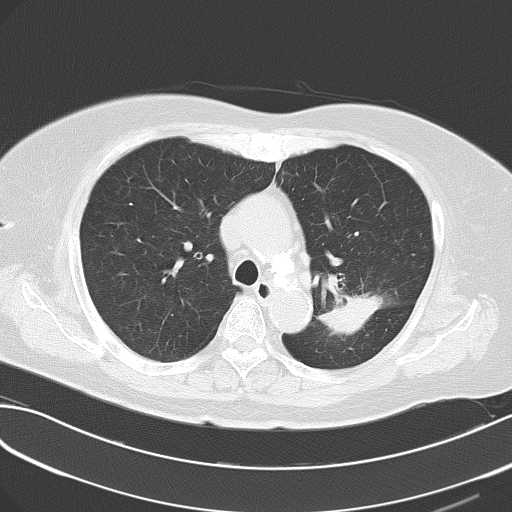
Chest CT, one axial slice. Slice 48 of 62 in the series (ordered by position). Reconstruction kernel B70f. Lung window (W 1500 / L -600 HU). 512 × 512 image matrix. Female patient, age 70 years. From the clinical record (not read from this slice): clinical TNM (as recorded): T2 N0 M0.
Outlined on this slice (rectangle marked by the reading radiologist):
- lung tumour (recorded histology: adenocarcinoma): box from (x=317, y=285) to (x=387, y=342) px